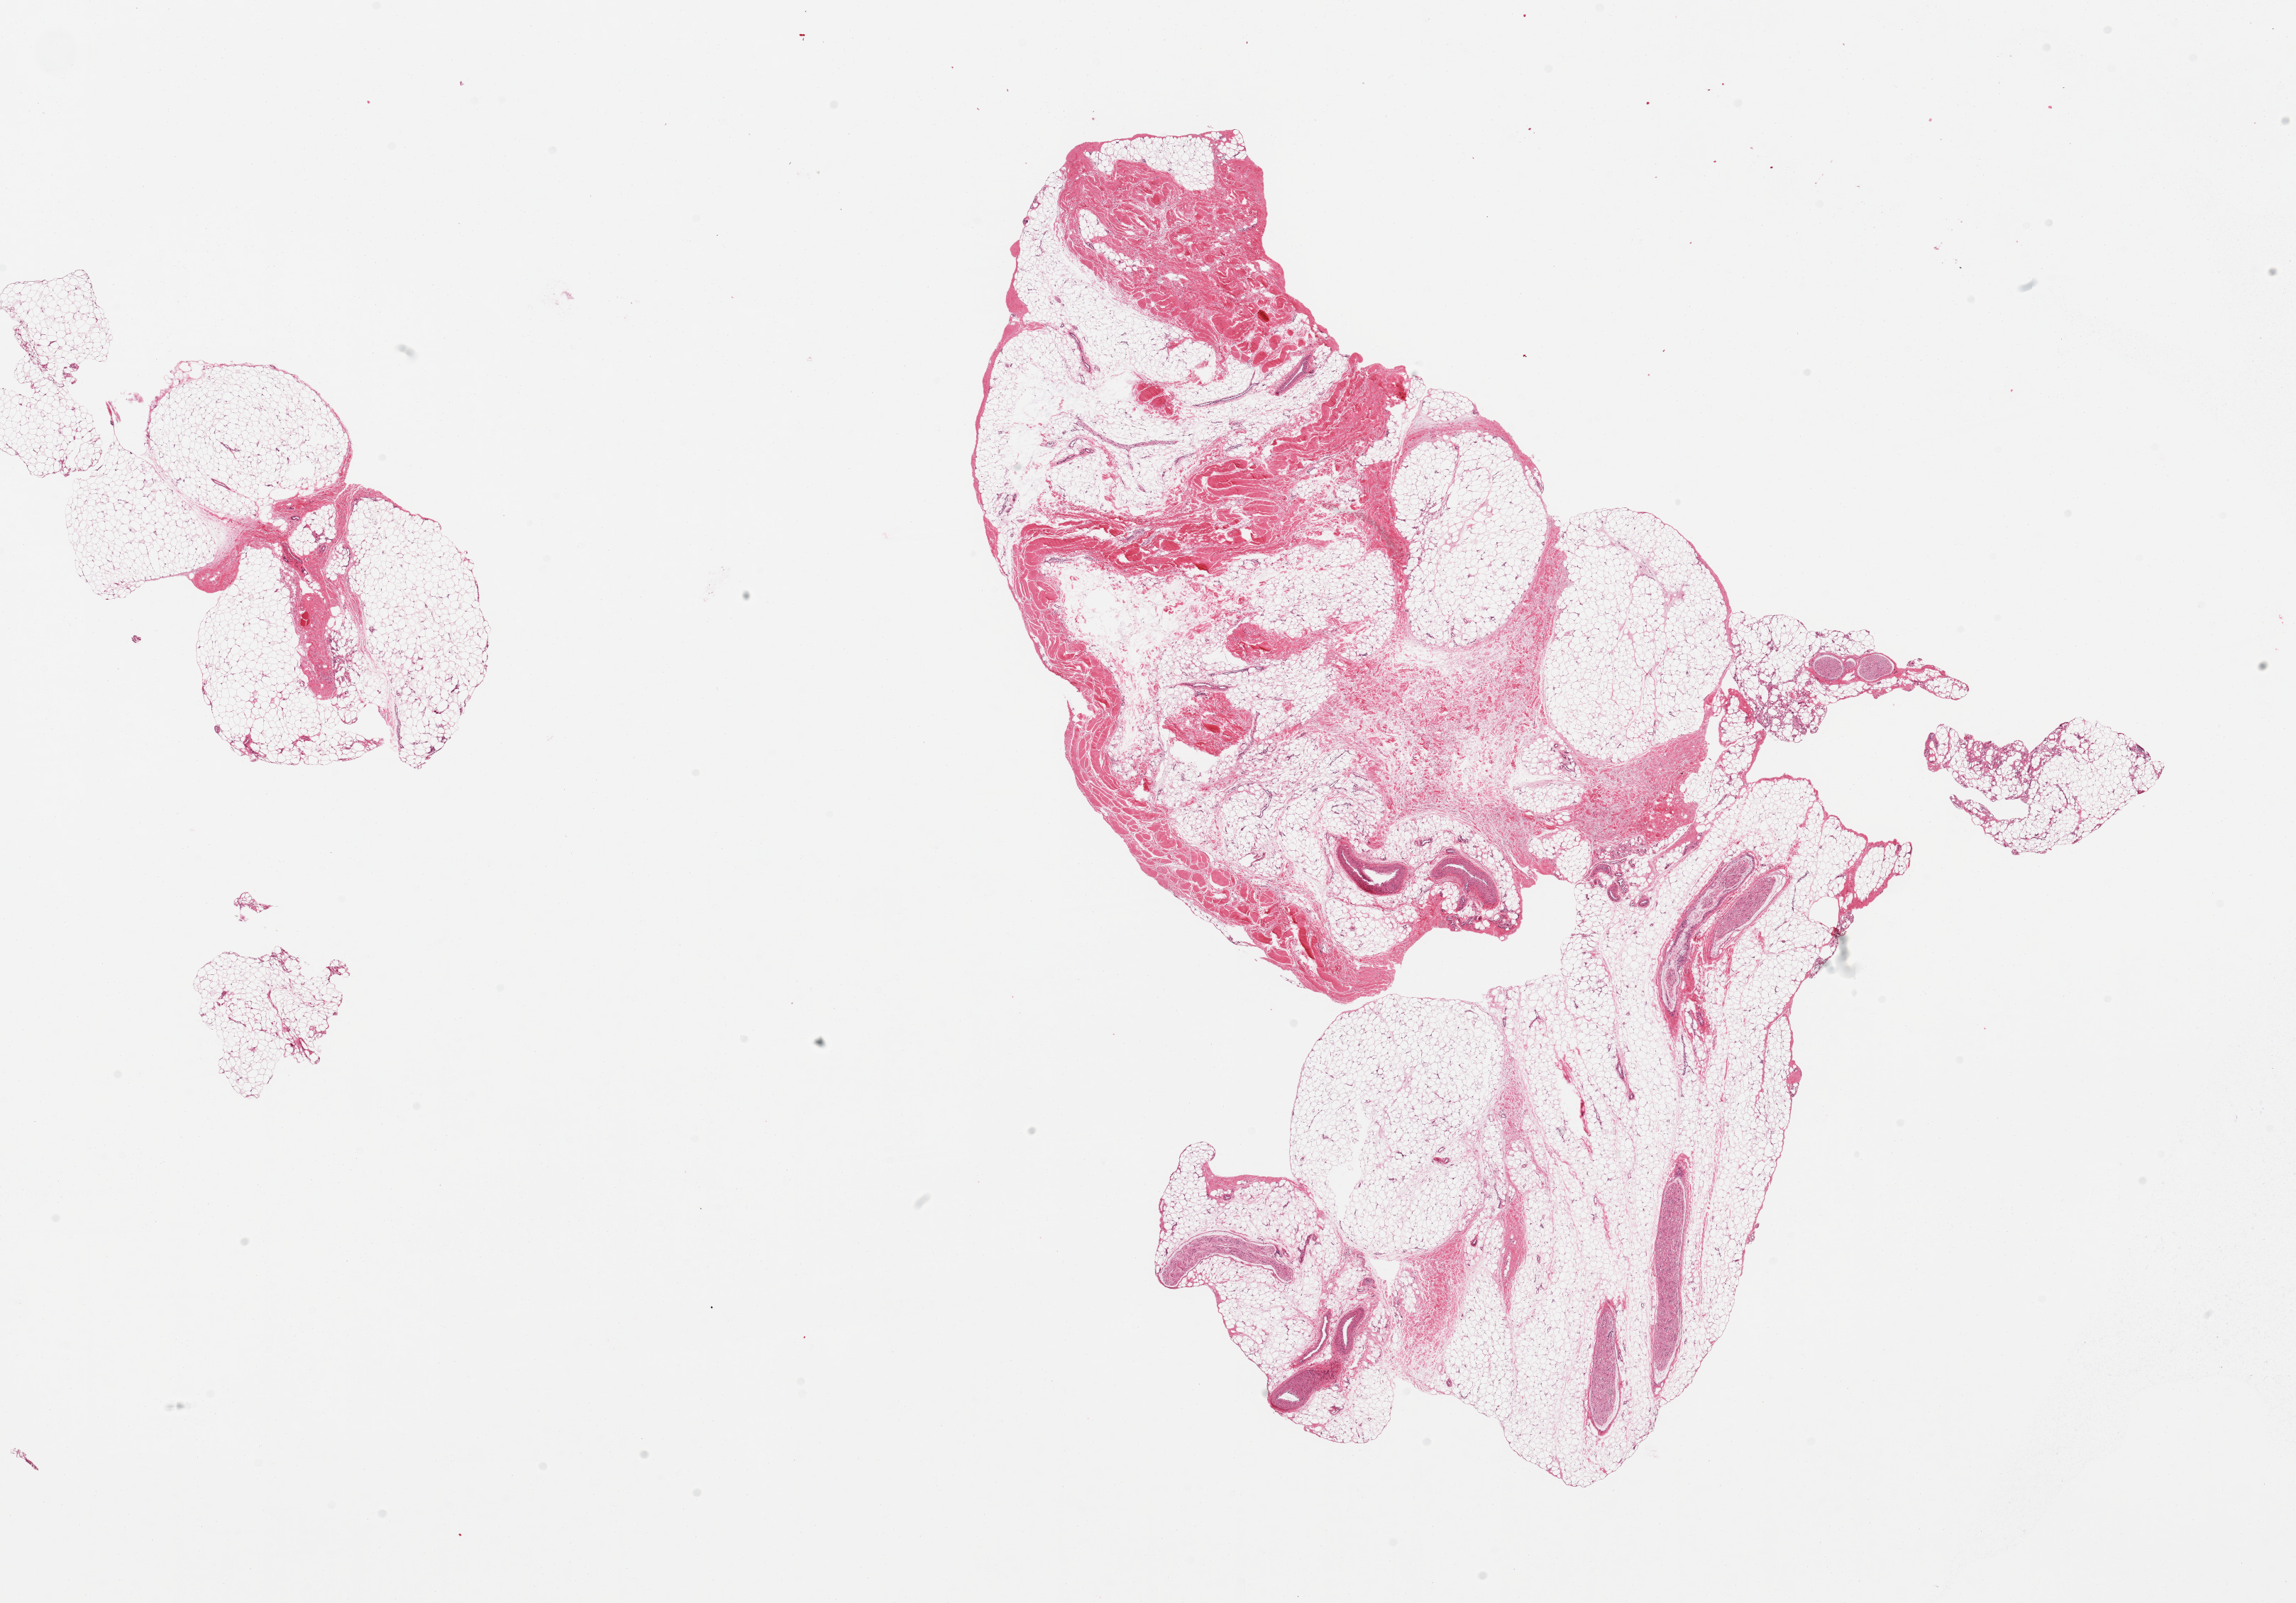
Whole-slide image, haematoxylin and eosin stain, brightfield — a low-resolution overview of the entire scanned area, about 25.6 x 17.9 mm. PAXgene-fixed, paraffin-embedded tissue. Section of adipose tissue (target tissue). Tissue donor sample.
Review note (as recorded): 2 pieces; includes significant portion of nerve, larger vessels and tendon.